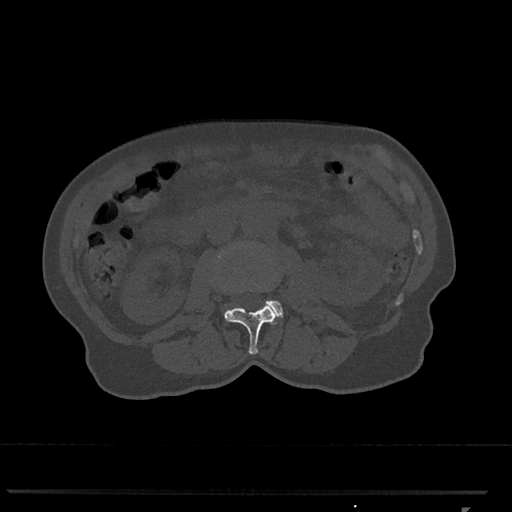
CT including the spine, one axial slice; slice 313 of 793 in the series (ordered by position); reconstruction kernel Br40s/3; 120 kVp; bone window (W 1800 / L 400 HU); 0.5 mm slice thickness; 512 × 512 image matrix, field of view 380 × 380 mm. Patient: female, 62 years. From the clinical record (not read from this slice): primary cancer: renal.
Structures marked on this image (semi-automatic segmentation, software-assisted and operator-edited):
- L2 vertebra: bounding box [x1, y1, x2, y2] px = [219, 256, 278, 354]
- L3 vertebra: [266, 300, 283, 318]